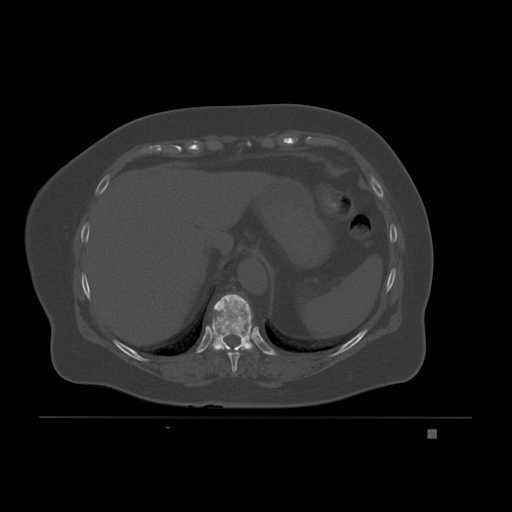
CT including the spine, one axial slice. Slice 103 of 221 in the series (ordered by position). Bone window (W 1800 / L 400 HU). 3 mm slice thickness. 512 × 512 image matrix. Patient: female, 63 years. From the clinical record (not read from this slice): primary cancer: breast.
Annotated regions visible in this slice (semi-automatically segmented with operator editing):
- T10 vertebra: box from (x=211, y=294) to (x=253, y=352) px
- T9 vertebra: (x=218, y=345)–(x=249, y=373)